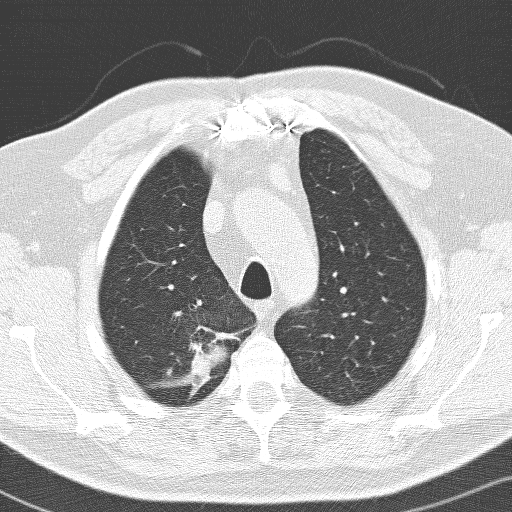
Low-dose screening chest CT, one axial slice. 120 kVp. Lung window (W 1500 / L -600 HU). 3.2 mm slice thickness. 512 × 512 image matrix.
Annotated regions visible in this slice (expert manual segmentation):
- lesion 1 (tumor, upper lobe of right lung): bounding box [x1, y1, x2, y2] px = [188, 325, 238, 398]